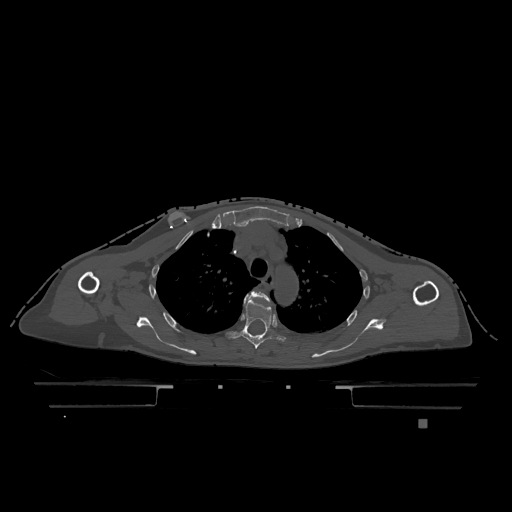
CT including the spine, one axial slice. Position 886 of 1317 along the scan axis. Bone window (W 1800 / L 400 HU). 0.5 mm slice thickness. 512 × 512 image matrix, field of view 500 × 500 mm. Patient: female, 74 years. From the clinical record (not read from this slice): primary cancer: lung; vertebrae with lytic lesions (as recorded): T1, T4, T5, T6, L4, L5.
Structures marked on this image (semi-automatic segmentation, software-assisted and operator-edited):
- T3 vertebra: bounding box (x1, y1, x2, y2) in pixels: (244, 291, 270, 303)
- T4 vertebra: (225, 298, 286, 349)